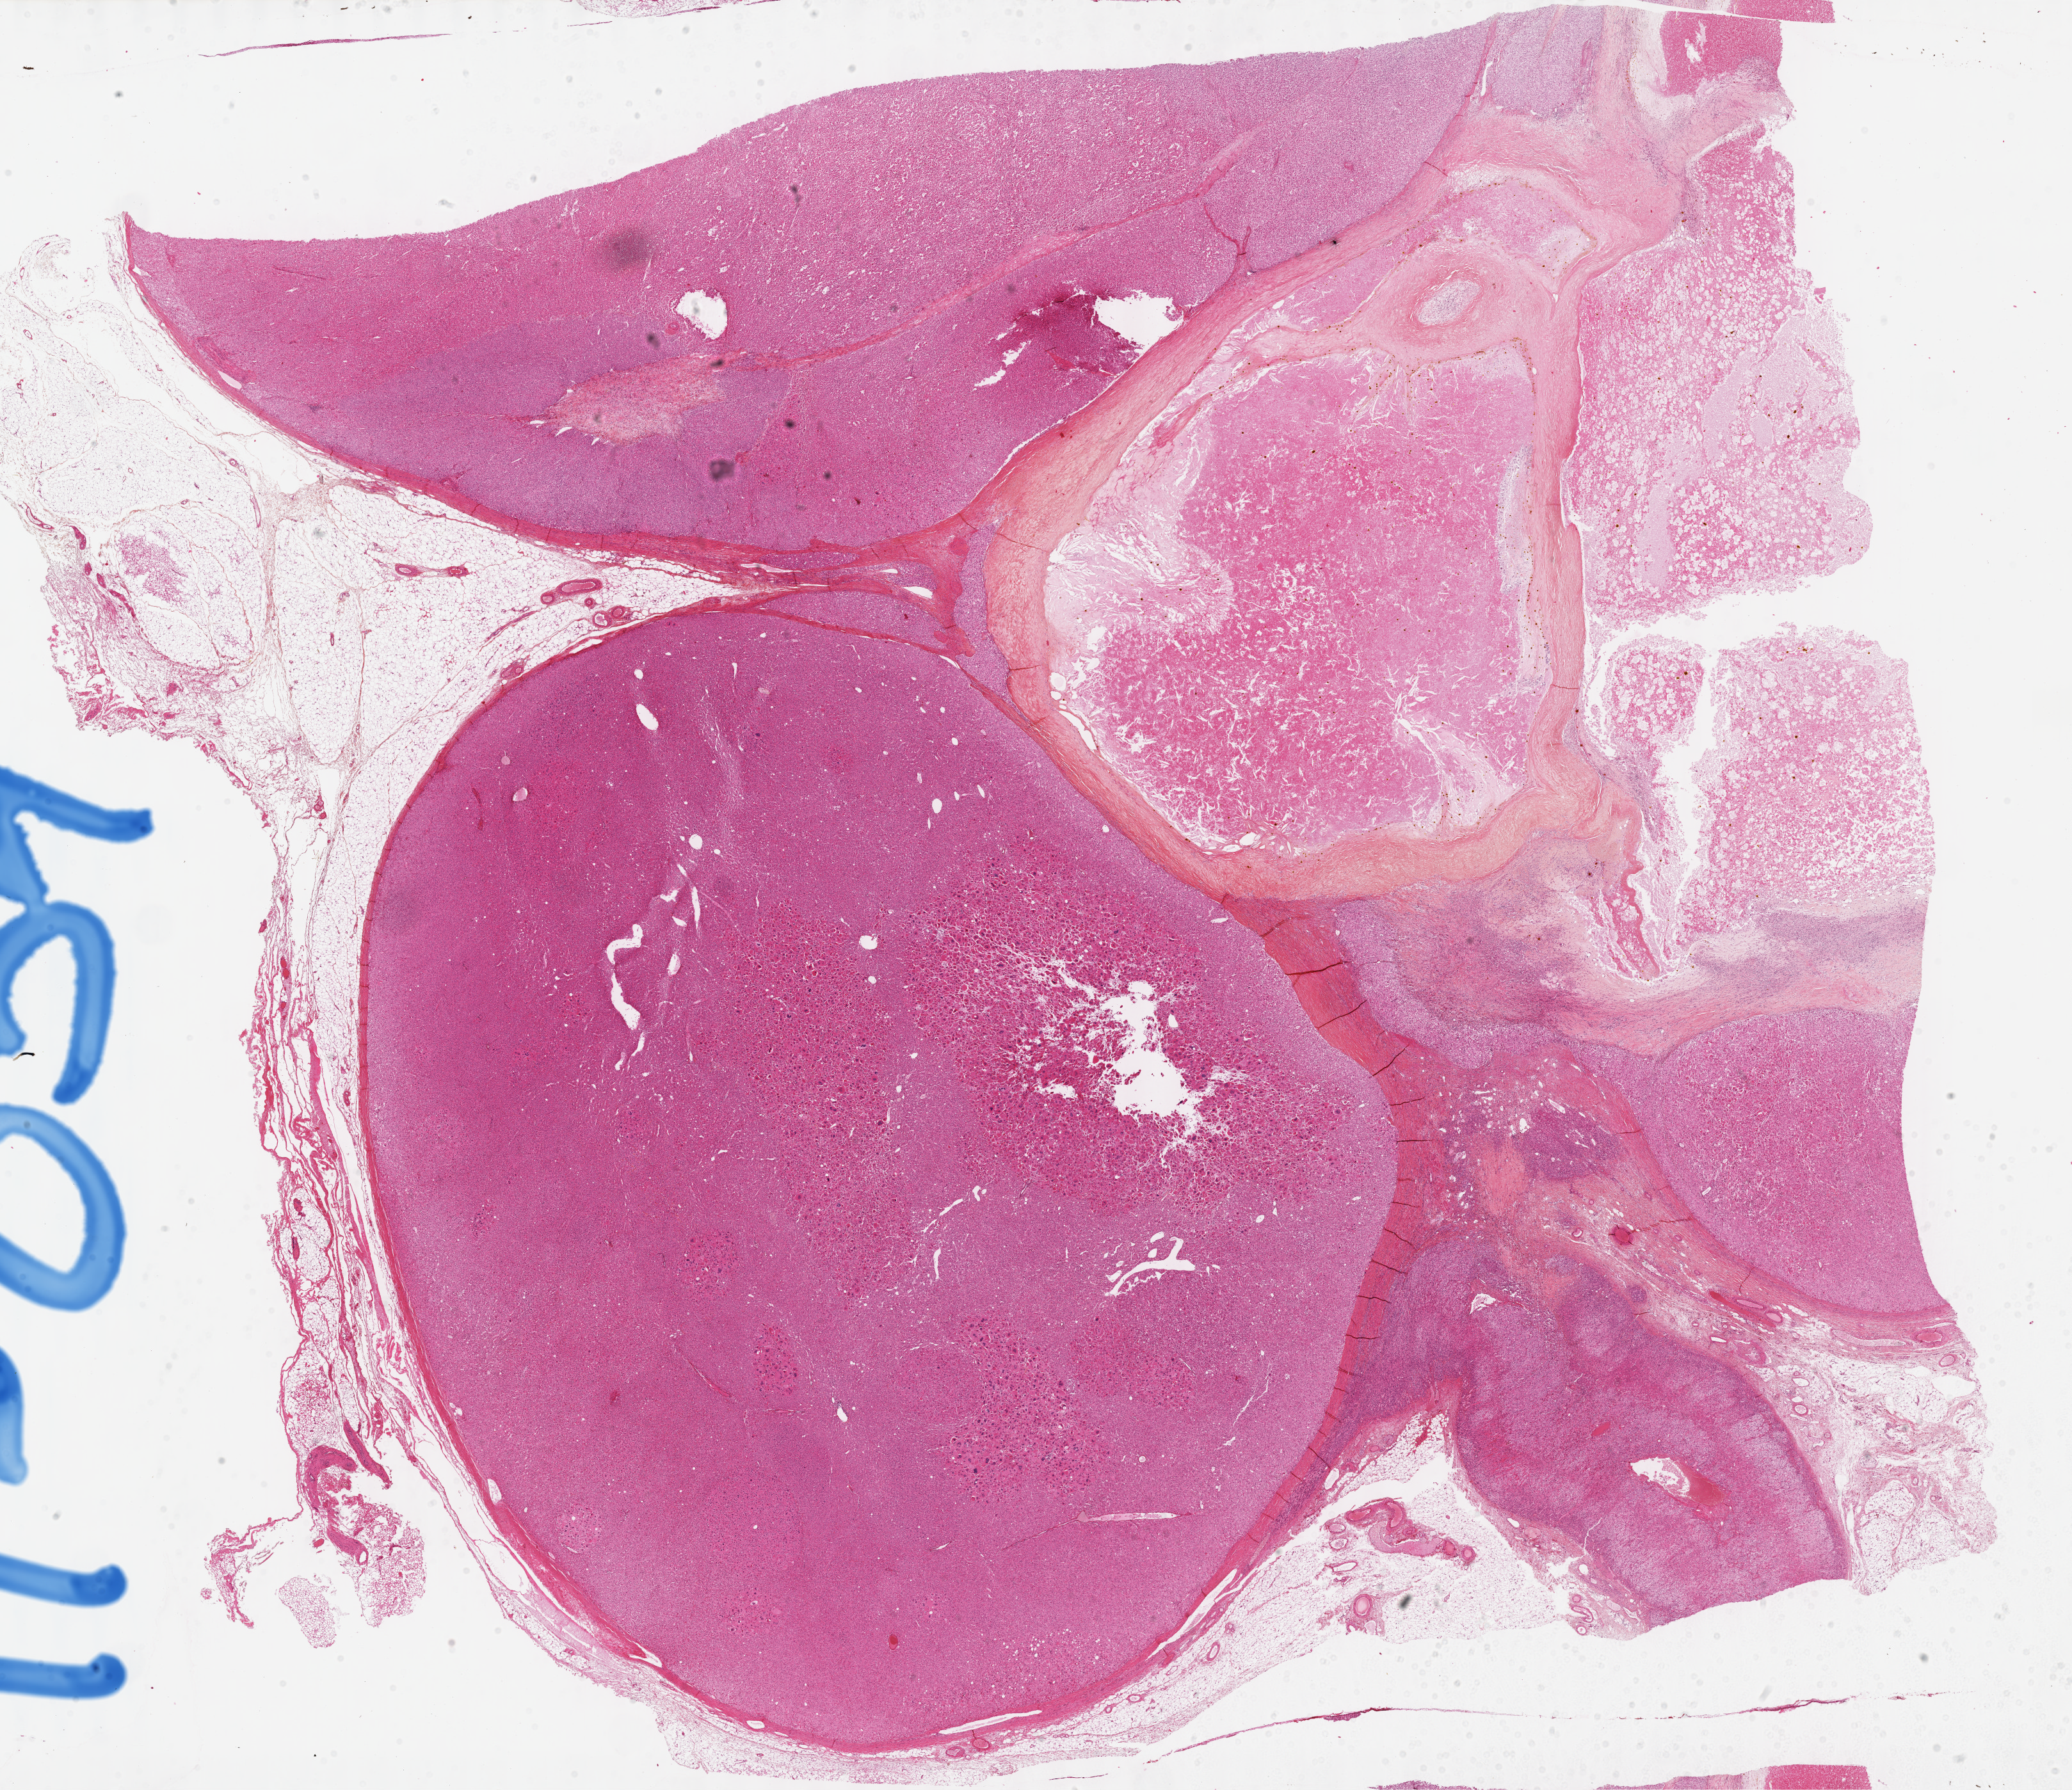
Digitized H&E tissue section (whole slide), shown as a low-resolution overview of the whole scanned area (about 26.2 x 22.6 mm, slide scanned at 40x). Formalin-fixed paraffin-embedded (FFPE) diagnostic section. Sample: primary tumour, adrenal cortex. Female patient; age at initial diagnosis 30 years.
Laterality: left. Diagnosis: Adrenal cortical carcinoma (cortex of adrenal gland).